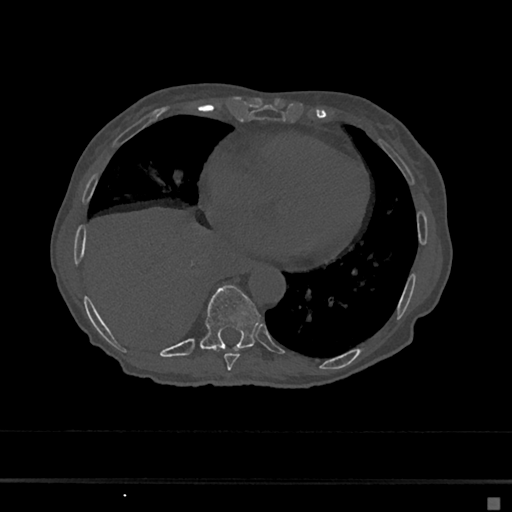
CT including the spine, one axial slice. Slice 291 of 797 in the series (ordered by position). Reconstruction kernel Br40s/3. 120 kVp. Bone window (W 1800 / L 400 HU). 512 × 512 image matrix, field of view 360 × 360 mm. Female patient, age 68 years. From the clinical record (not read from this slice): primary cancer: renal.
Structures marked on this image (semi-automatic segmentation, software-assisted and operator-edited):
- T8 vertebra: bounding box <224,353,240,371> (left, top, right, bottom; pixels)
- T9 vertebra: <200,285,260,351>